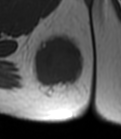
MRI of an extremity soft-tissue mass, one axial slice; slice 19 of 47 in the series (ordered by position); MR volume resampled by the dataset authors to the PET/CT grid (not the native acquisition matrix); 121 × 139 image matrix, field of view 118 × 136 mm. Female patient. Case-level facts recorded for this patient, not image findings: histological type: epithelioid sarcoma; grade: intermediate; site of the primary tumour: right buttock.
Structures marked on this image (expert contour drawn on MRI and transferred to this co-registered scan by the dataset authors):
- gross tumour volume including surrounding oedema: bounding box <29,34,87,106> (left, top, right, bottom; pixels)
- gross tumour volume (mass): <34,39,81,87>